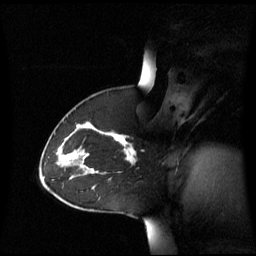
Breast MRI (dynamic contrast-enhanced), one sagittal slice. Slice 41 of 60 in the series (ordered by position). Dynamic contrast-enhanced series, image 2 of 3 at this slice position (ordered by acquisition). 1.5 T. TE 4.2 ms, TR 8.4 ms. 2.8 mm slice thickness. 256 × 256 image matrix. Female patient, age 43 years. Case-level facts recorded for this patient, not image findings: setting: breast cancer imaged before/during neoadjuvant chemotherapy; receptor status: triple-negative.
Annotated regions visible in this slice (semi-automatic segmentation, software-assisted and operator-edited):
- analysis volume of interest (the breast-tissue region the enhancement analysis was run in; not a lesion): bounding box [x1, y1, x2, y2] px = [55, 124, 137, 173]
- tumour enhancement mask (voxels above the 70 % enhancement threshold inside the analysis volume of interest): [70, 134, 136, 162]